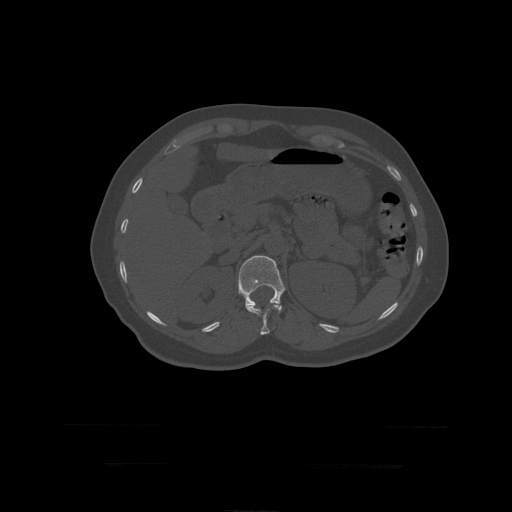
CT including the spine, one axial slice; slice 184 of 399 in the series (ordered by position); 120 kVp; bone window (W 1800 / L 400 HU); 1.25 mm slice thickness; 512 × 512 image matrix. Patient age 41 years. From the clinical record (not read from this slice): primary cancer: breast.
Structures marked on this image (semi-automatic segmentation, software-assisted and operator-edited):
- L1 vertebra: box from (x=238, y=256) to (x=286, y=313) px
- T12 vertebra: (x=246, y=304)–(x=281, y=335)